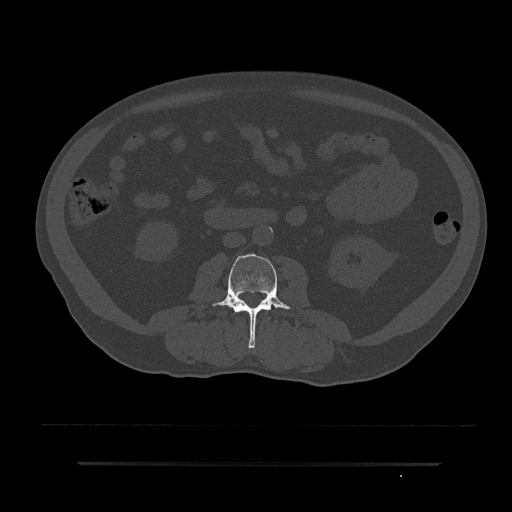
CT including the spine, one axial slice; slice 6 of 797 in the series (ordered by position); reconstruction kernel Br40s/3; 120 kVp; bone window (W 1800 / L 400 HU); 0.5 mm slice thickness; 512 × 512 image matrix, field of view 464 × 464 mm. Male patient, age 59 years. Case-level facts recorded for this patient, not image findings: primary cancer: bile ducts.
Outlined on this slice (semi-automatic segmentation, software-assisted and operator-edited):
- L2 vertebra: bounding box [x1, y1, x2, y2] px = [242, 310, 249, 313]
- L3 vertebra: [202, 254, 294, 348]